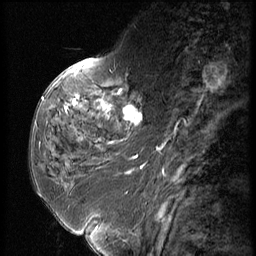
Breast MRI (dynamic contrast-enhanced), one sagittal slice; slice 20 of 56 in the series (ordered by position); dynamic contrast-enhanced series, image 2 of 3 at this slice position (ordered by acquisition); 1.5 T; TE 4.2 ms, TR 9 ms; 2.5 mm slice thickness; 256 × 256 image matrix, field of view 180 × 180 mm. Patient: female, 59 years. From the clinical record (not read from this slice): setting: breast cancer imaged before/during neoadjuvant chemotherapy; receptor status: HER2-positive.
Annotated regions visible in this slice (semi-automatically segmented with operator editing):
- analysis volume of interest (the breast-tissue region the enhancement analysis was run in; not a lesion): bounding box [x1, y1, x2, y2] px = [44, 66, 151, 135]
- tumour enhancement mask (voxels above the 140 % enhancement threshold inside the analysis volume of interest): [65, 95, 137, 120]